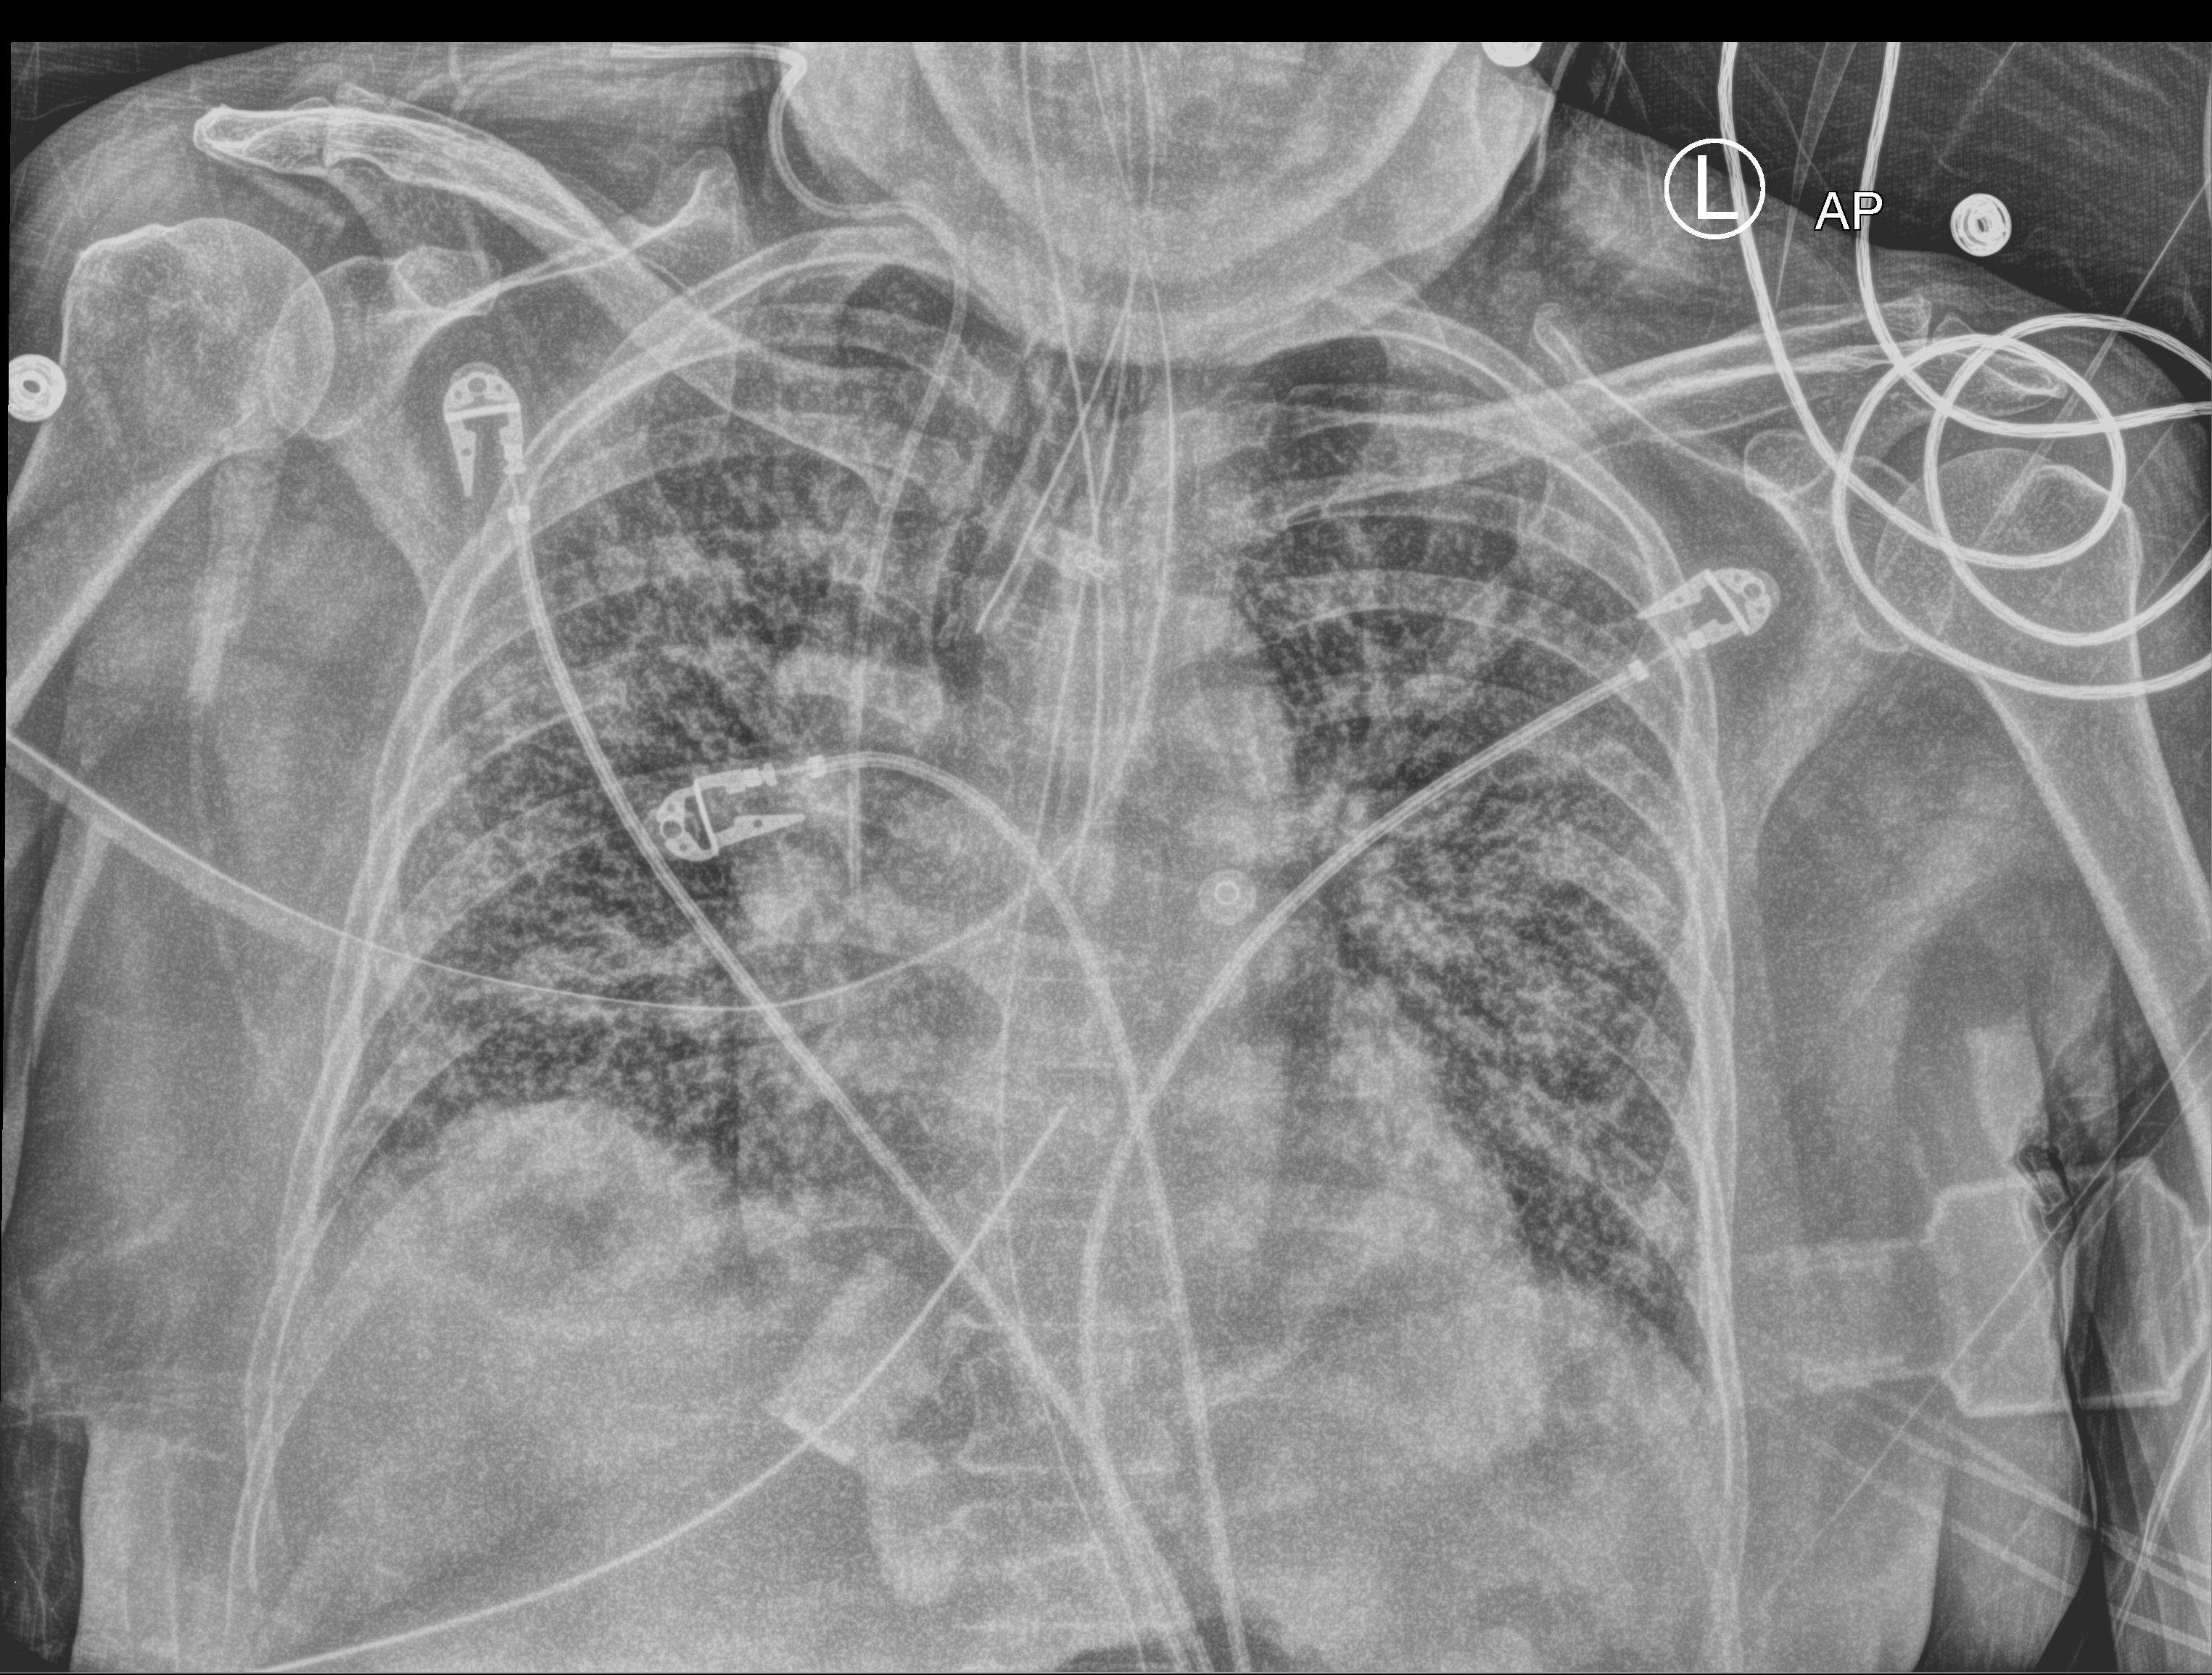
Bedside chest radiograph (computed radiography), anteroposterior (AP) projection. Patient hospitalised with COVID-19; female, aged 60–74 years.
Hospital-stay facts (about this admission, not read from this image; timing relative to this image not recorded): smoking status (admission record): never; mechanically ventilated during this hospital stay: yes; admitted to intensive care during this hospital stay: yes.